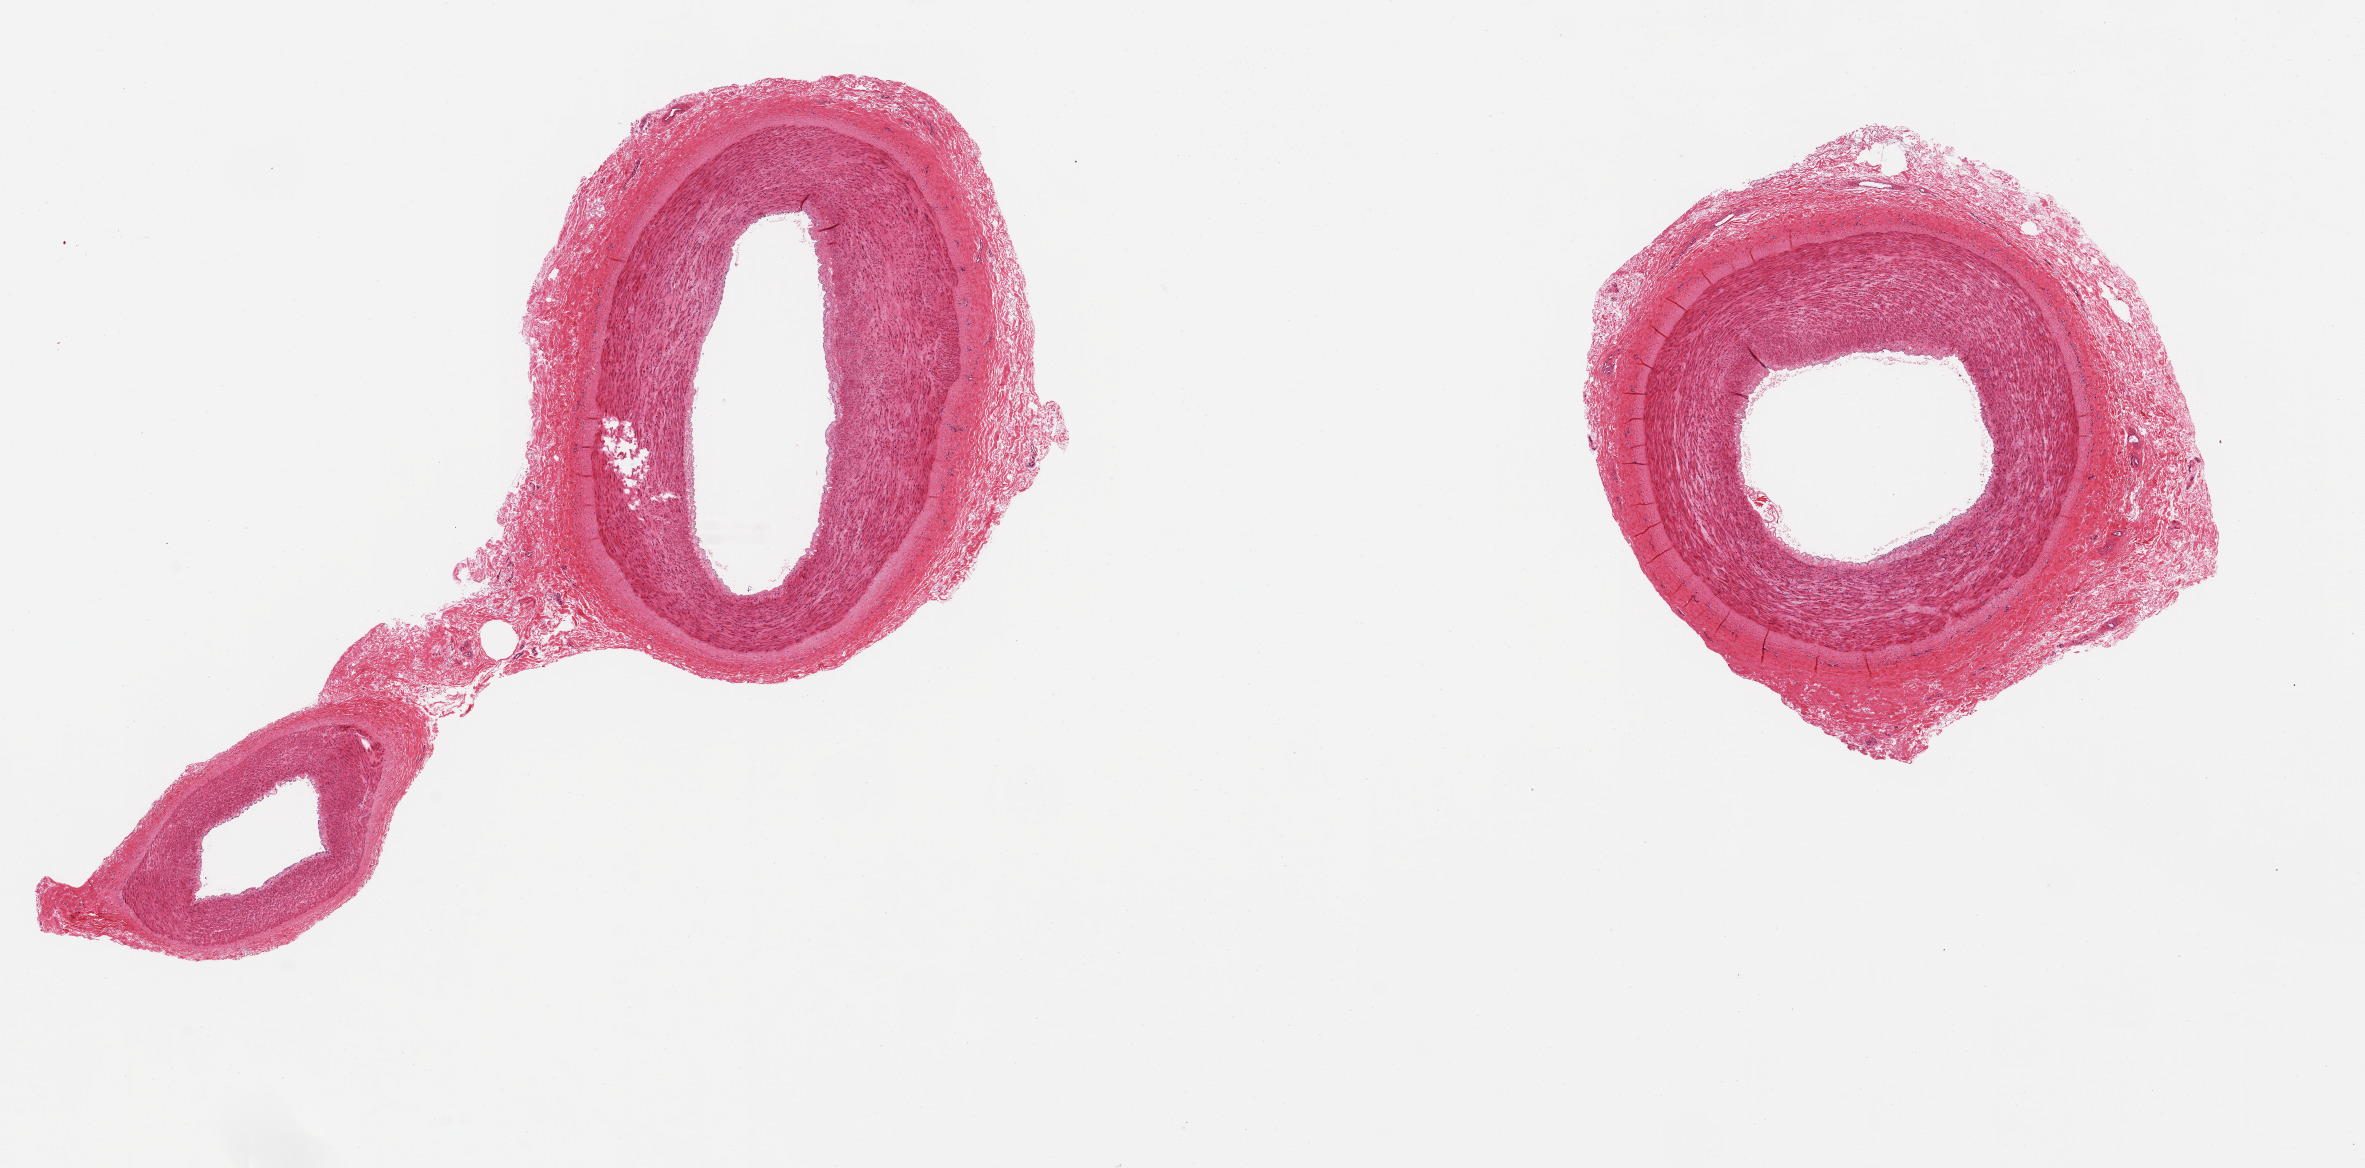
Hematoxylin and eosin (H&E) whole-slide image, a low-resolution overview of the entire scanned area, about 18.7 x 9.2 mm (acquisition: 20x scan); PAXgene-fixed paraffin-embedded (PFPE) section; sampled site (target tissue): tibial artery; donor tissue sample. Donor sex: male.
• pathologist's review note for this sample: 2 aliquots, ~4.5mm d. Fairly clean specimens